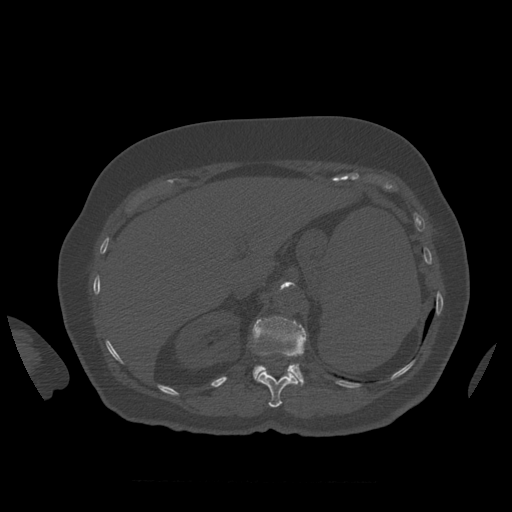
CT including the spine, one axial slice. Slice 291 of 399 in the series (ordered by position). Bone window (W 1800 / L 400 HU). 1.25 mm slice thickness. 512 × 512 image matrix. Patient age 81 years. Case-level facts recorded for this patient, not image findings: primary cancer: renal.
Structures marked on this image (semi-automatic segmentation, software-assisted and operator-edited):
- L1 vertebra: bounding box <253,317,307,386> (left, top, right, bottom; pixels)
- T12 vertebra: <257,372,298,408>